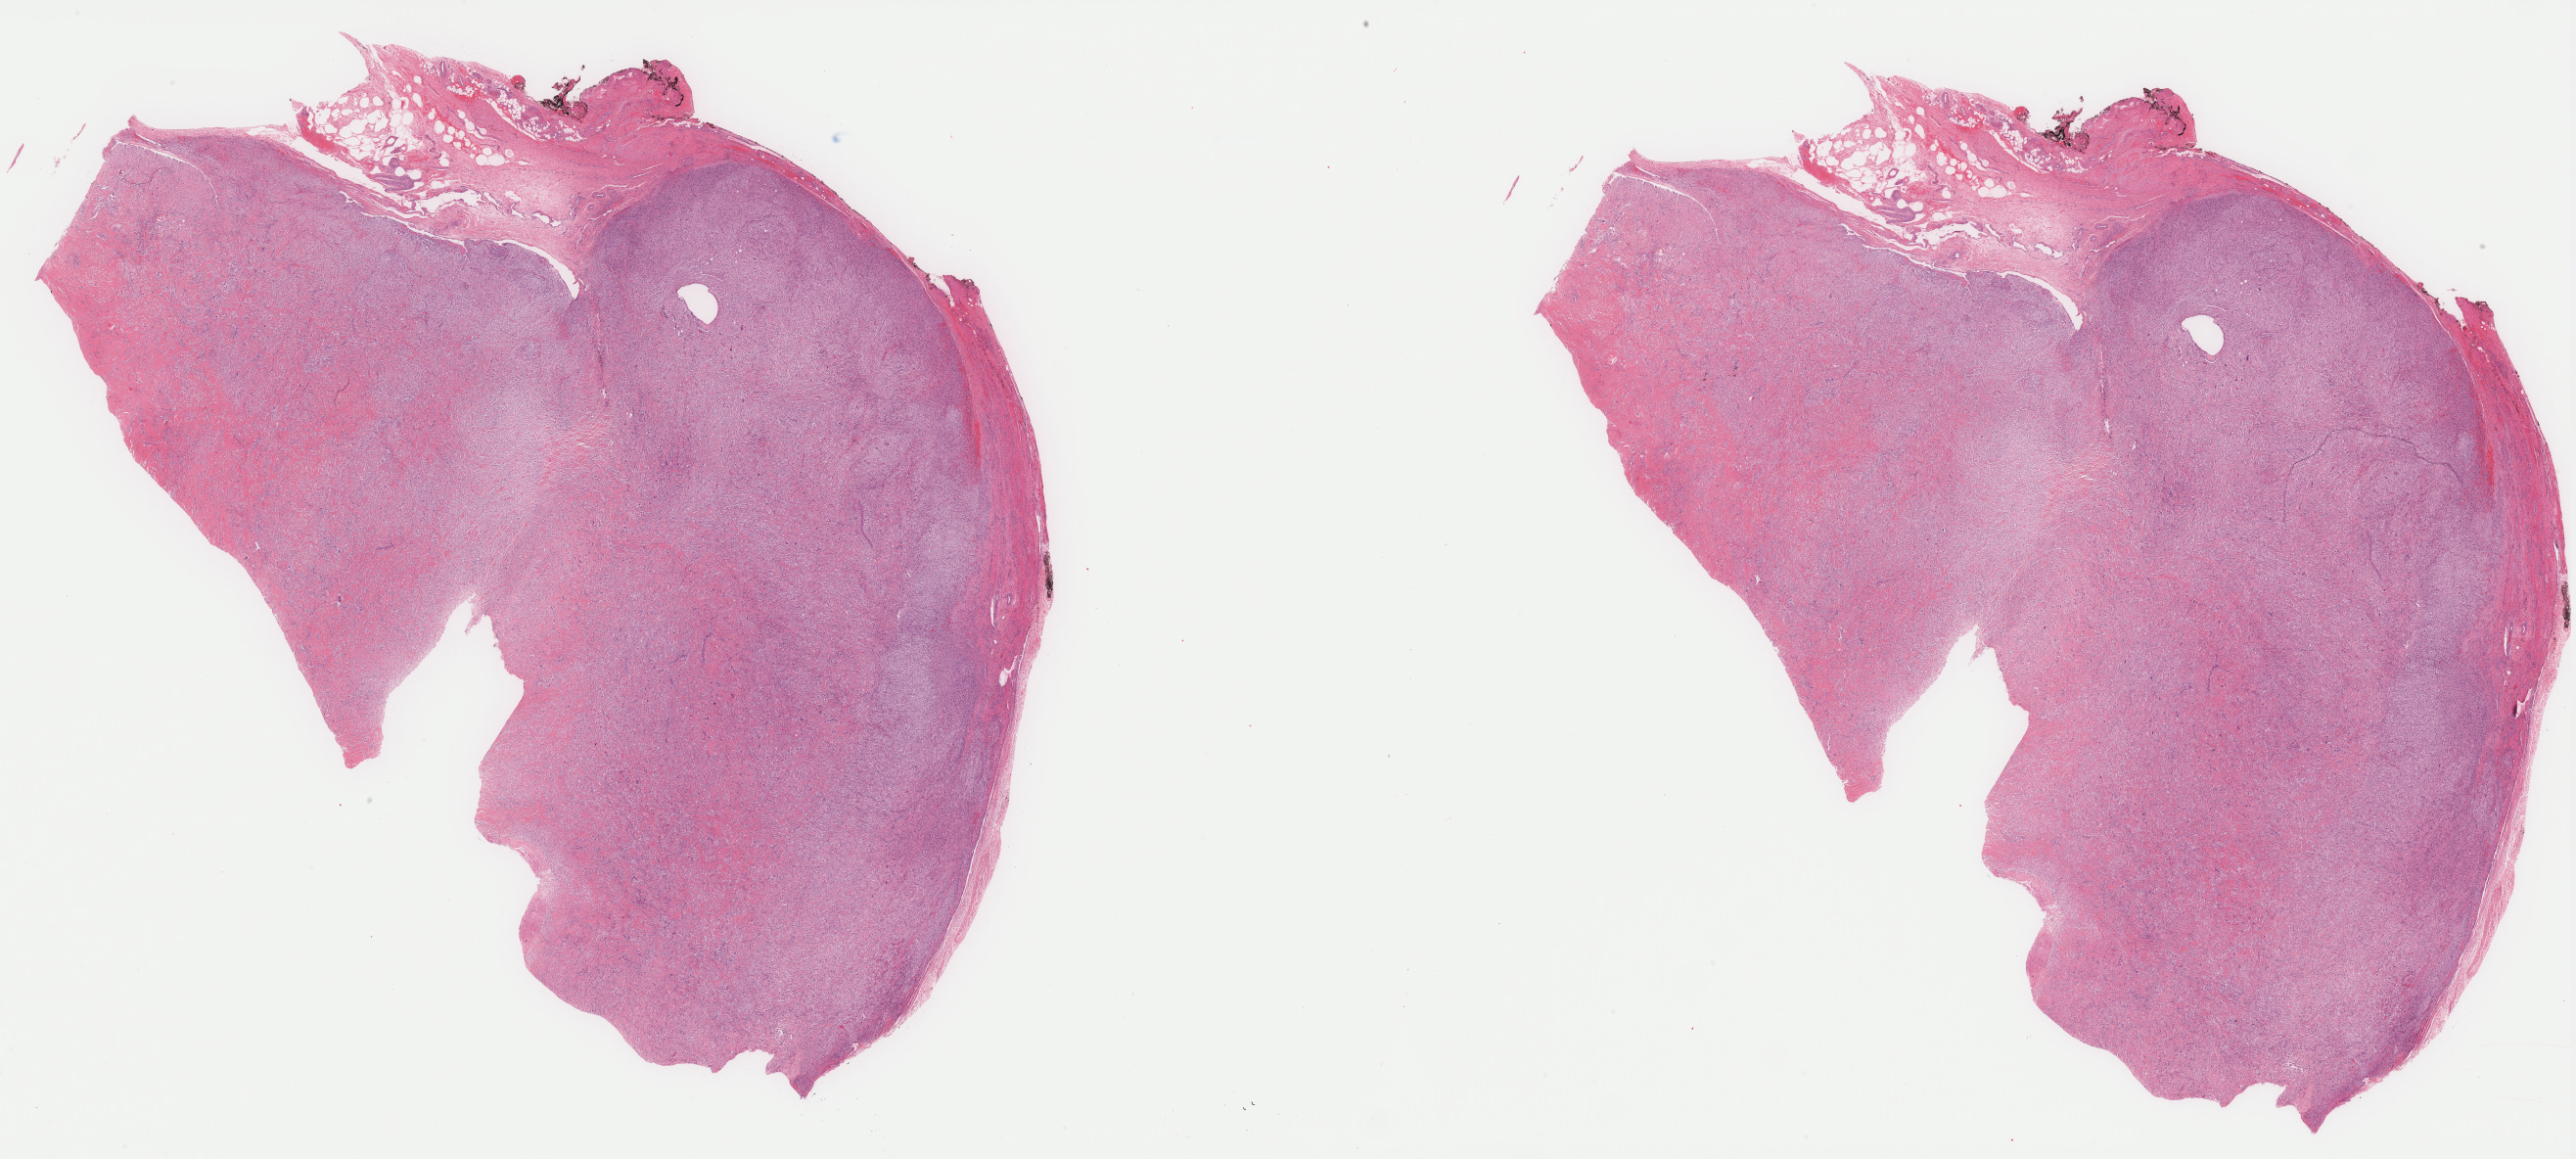
Whole-slide histology image, H&E-stained, shown as a low-resolution overview of the whole scanned area (about 42.1 x 18.9 mm, acquisition: 40x scan); formalin-fixed paraffin-embedded (FFPE) diagnostic section; sample: primary tumour, connective, subcutaneous and other soft tissues. Male, age 80 years at initial diagnosis.
Pathologic diagnosis: Liposarcoma, NOS (connective, subcutaneous and other soft tissues, NOS).